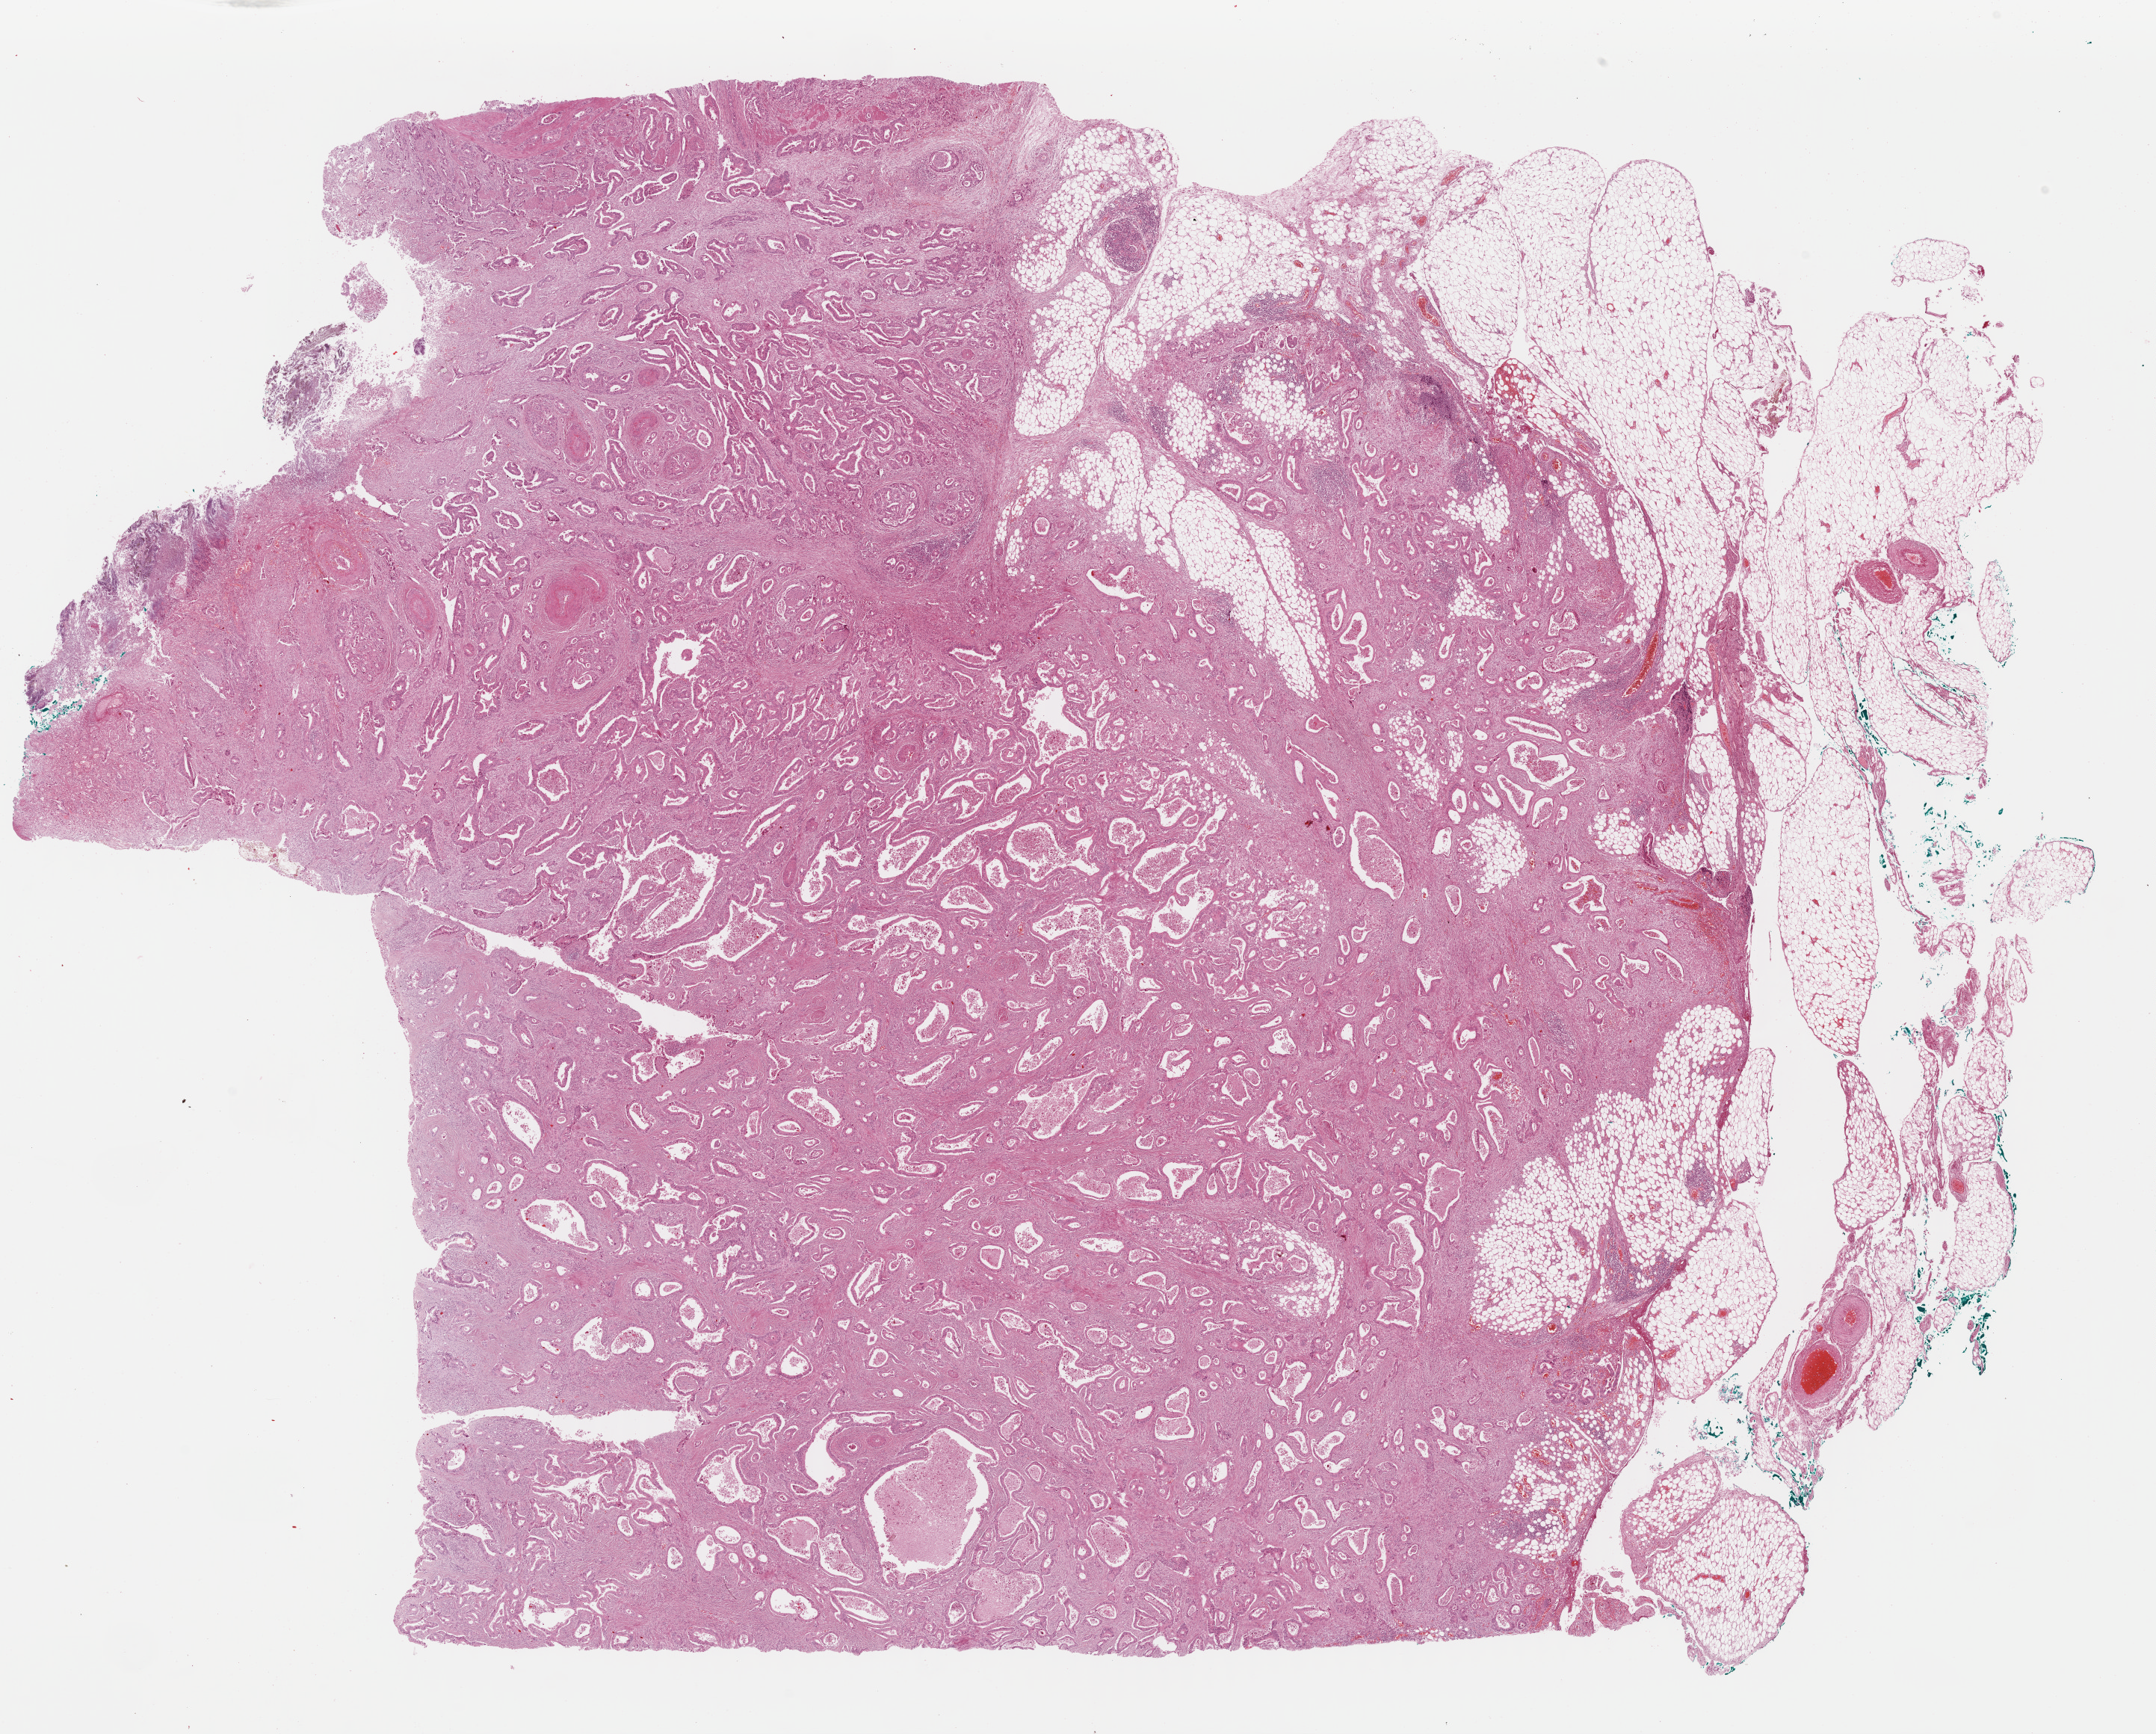
Digitized H&E tissue section (whole slide) — a low-resolution overview of the entire scanned area, about 22.7 x 18.2 mm (acquisition: 40x scan), formalin-fixed paraffin-embedded (FFPE) diagnostic section, primary tumour sample from the stomach. Patient: female, age at initial diagnosis 67 years. Histologic grade: G2 (moderately differentiated).
- AJCC pathologic stage: IIIA (7th edition)
- pathologic diagnosis: Tubular adenocarcinoma
- lymph nodes positive (case pathology): 3 of 19 examined